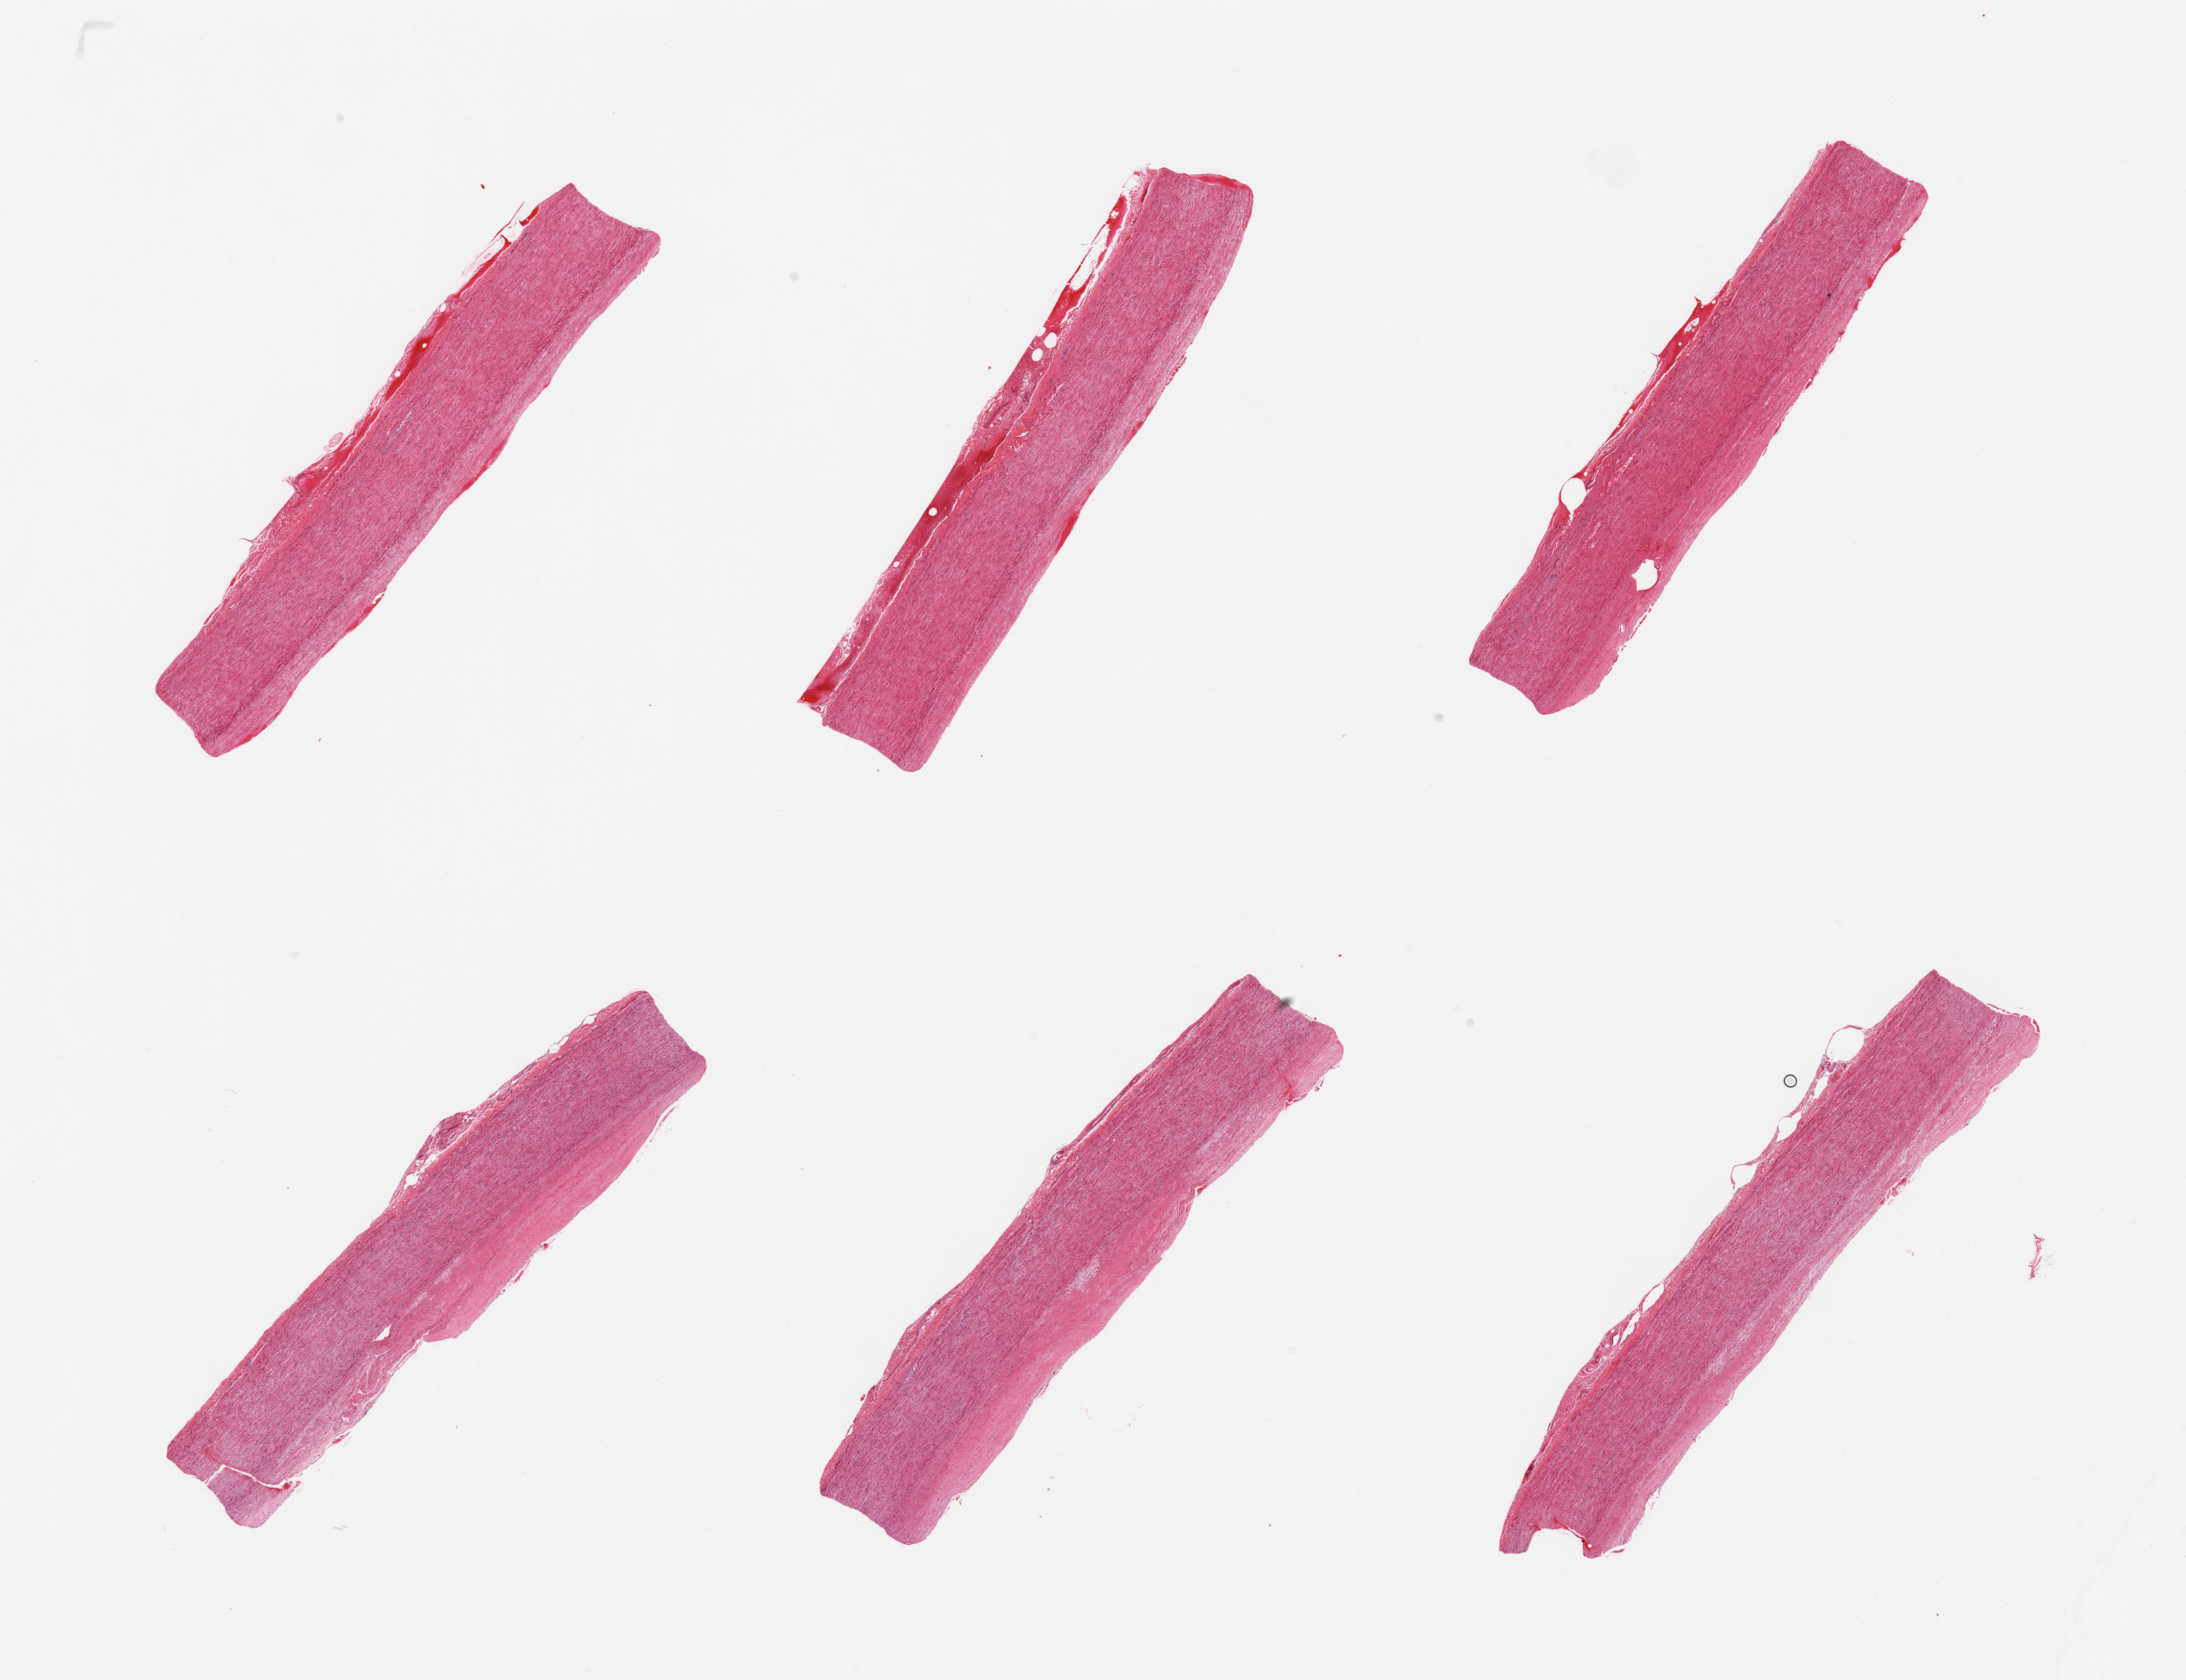
Whole-slide image, hematoxylin and eosin (H&E) stain, low-resolution overview of the scanned area, about 25.6 x 19.7 mm; PAXgene-fixed paraffin-embedded (PFPE) section; target tissue: aorta; donor tissue sample. Donor sex: female.
• reviewer comment on this tissue sample: 6 pieces, mild-moderate atherosis up to ~0.3mm noted